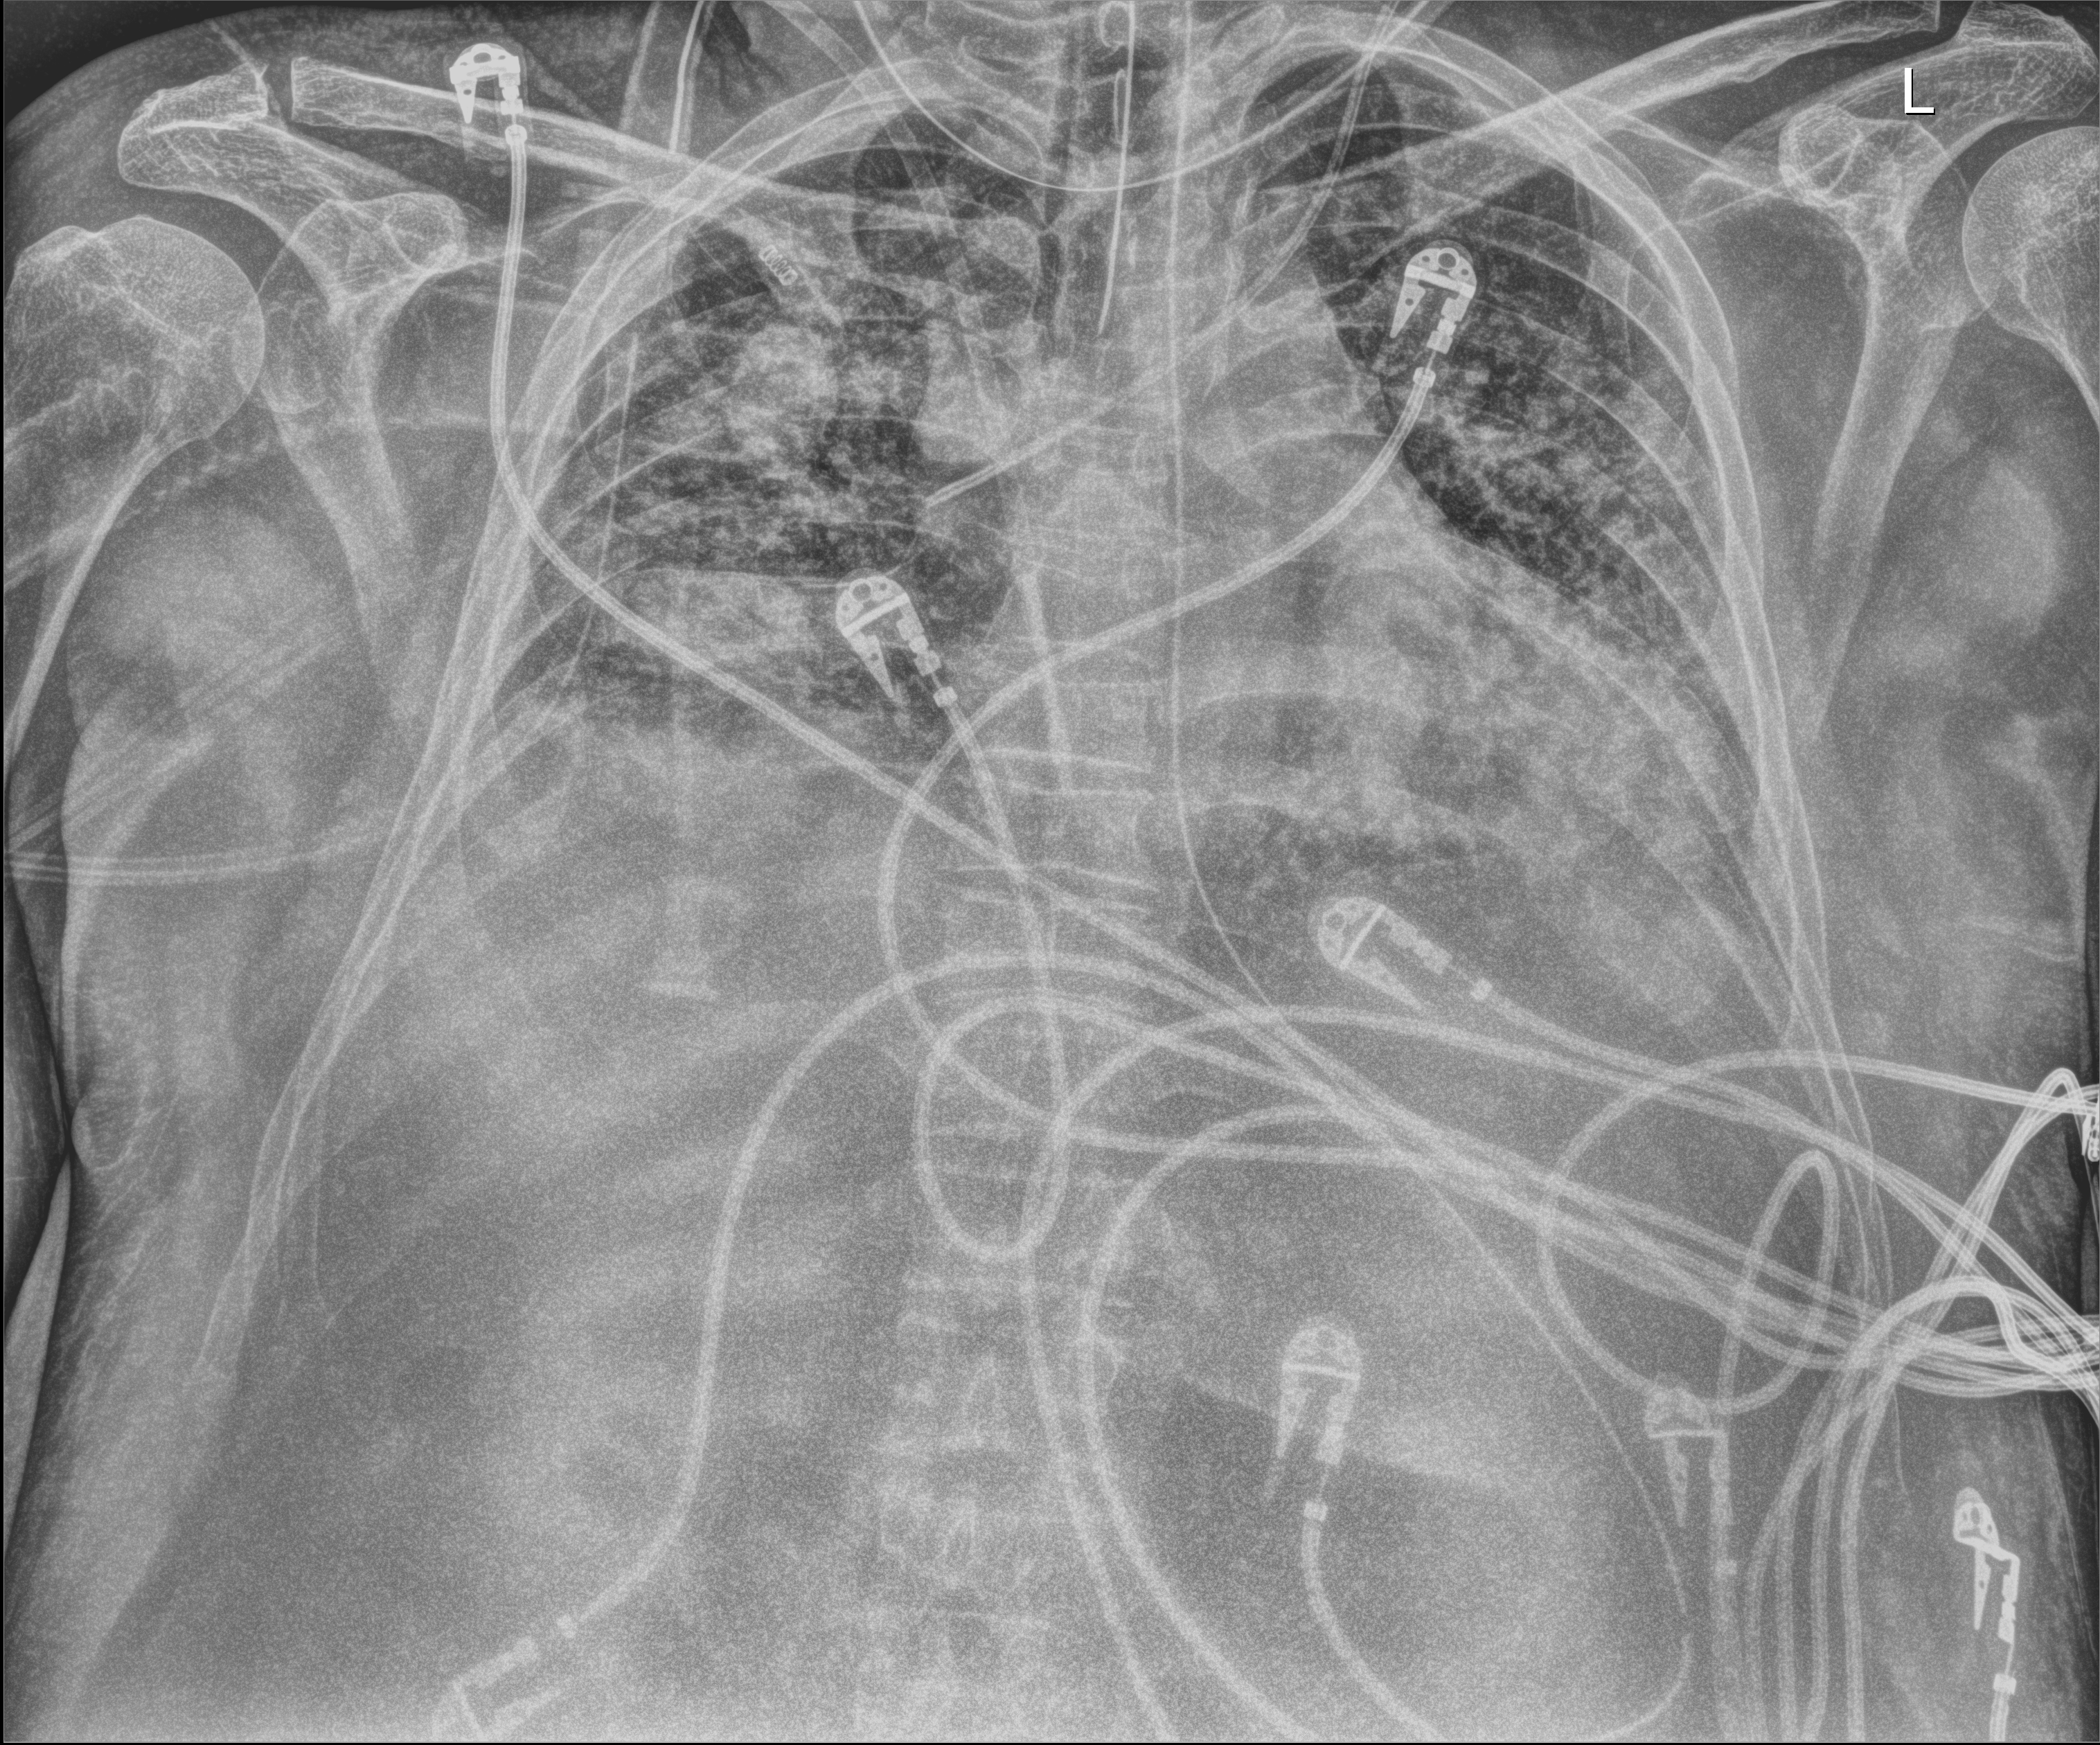
Bedside chest radiograph (digital radiography), anteroposterior (AP) projection. Male patient hospitalised with COVID-19, age 60–74 years.
From the hospital-stay record, not from the radiograph (when in the stay this image was taken is not recorded):
- diabetes (admission record): no
- admitted to intensive care during this hospital stay: yes